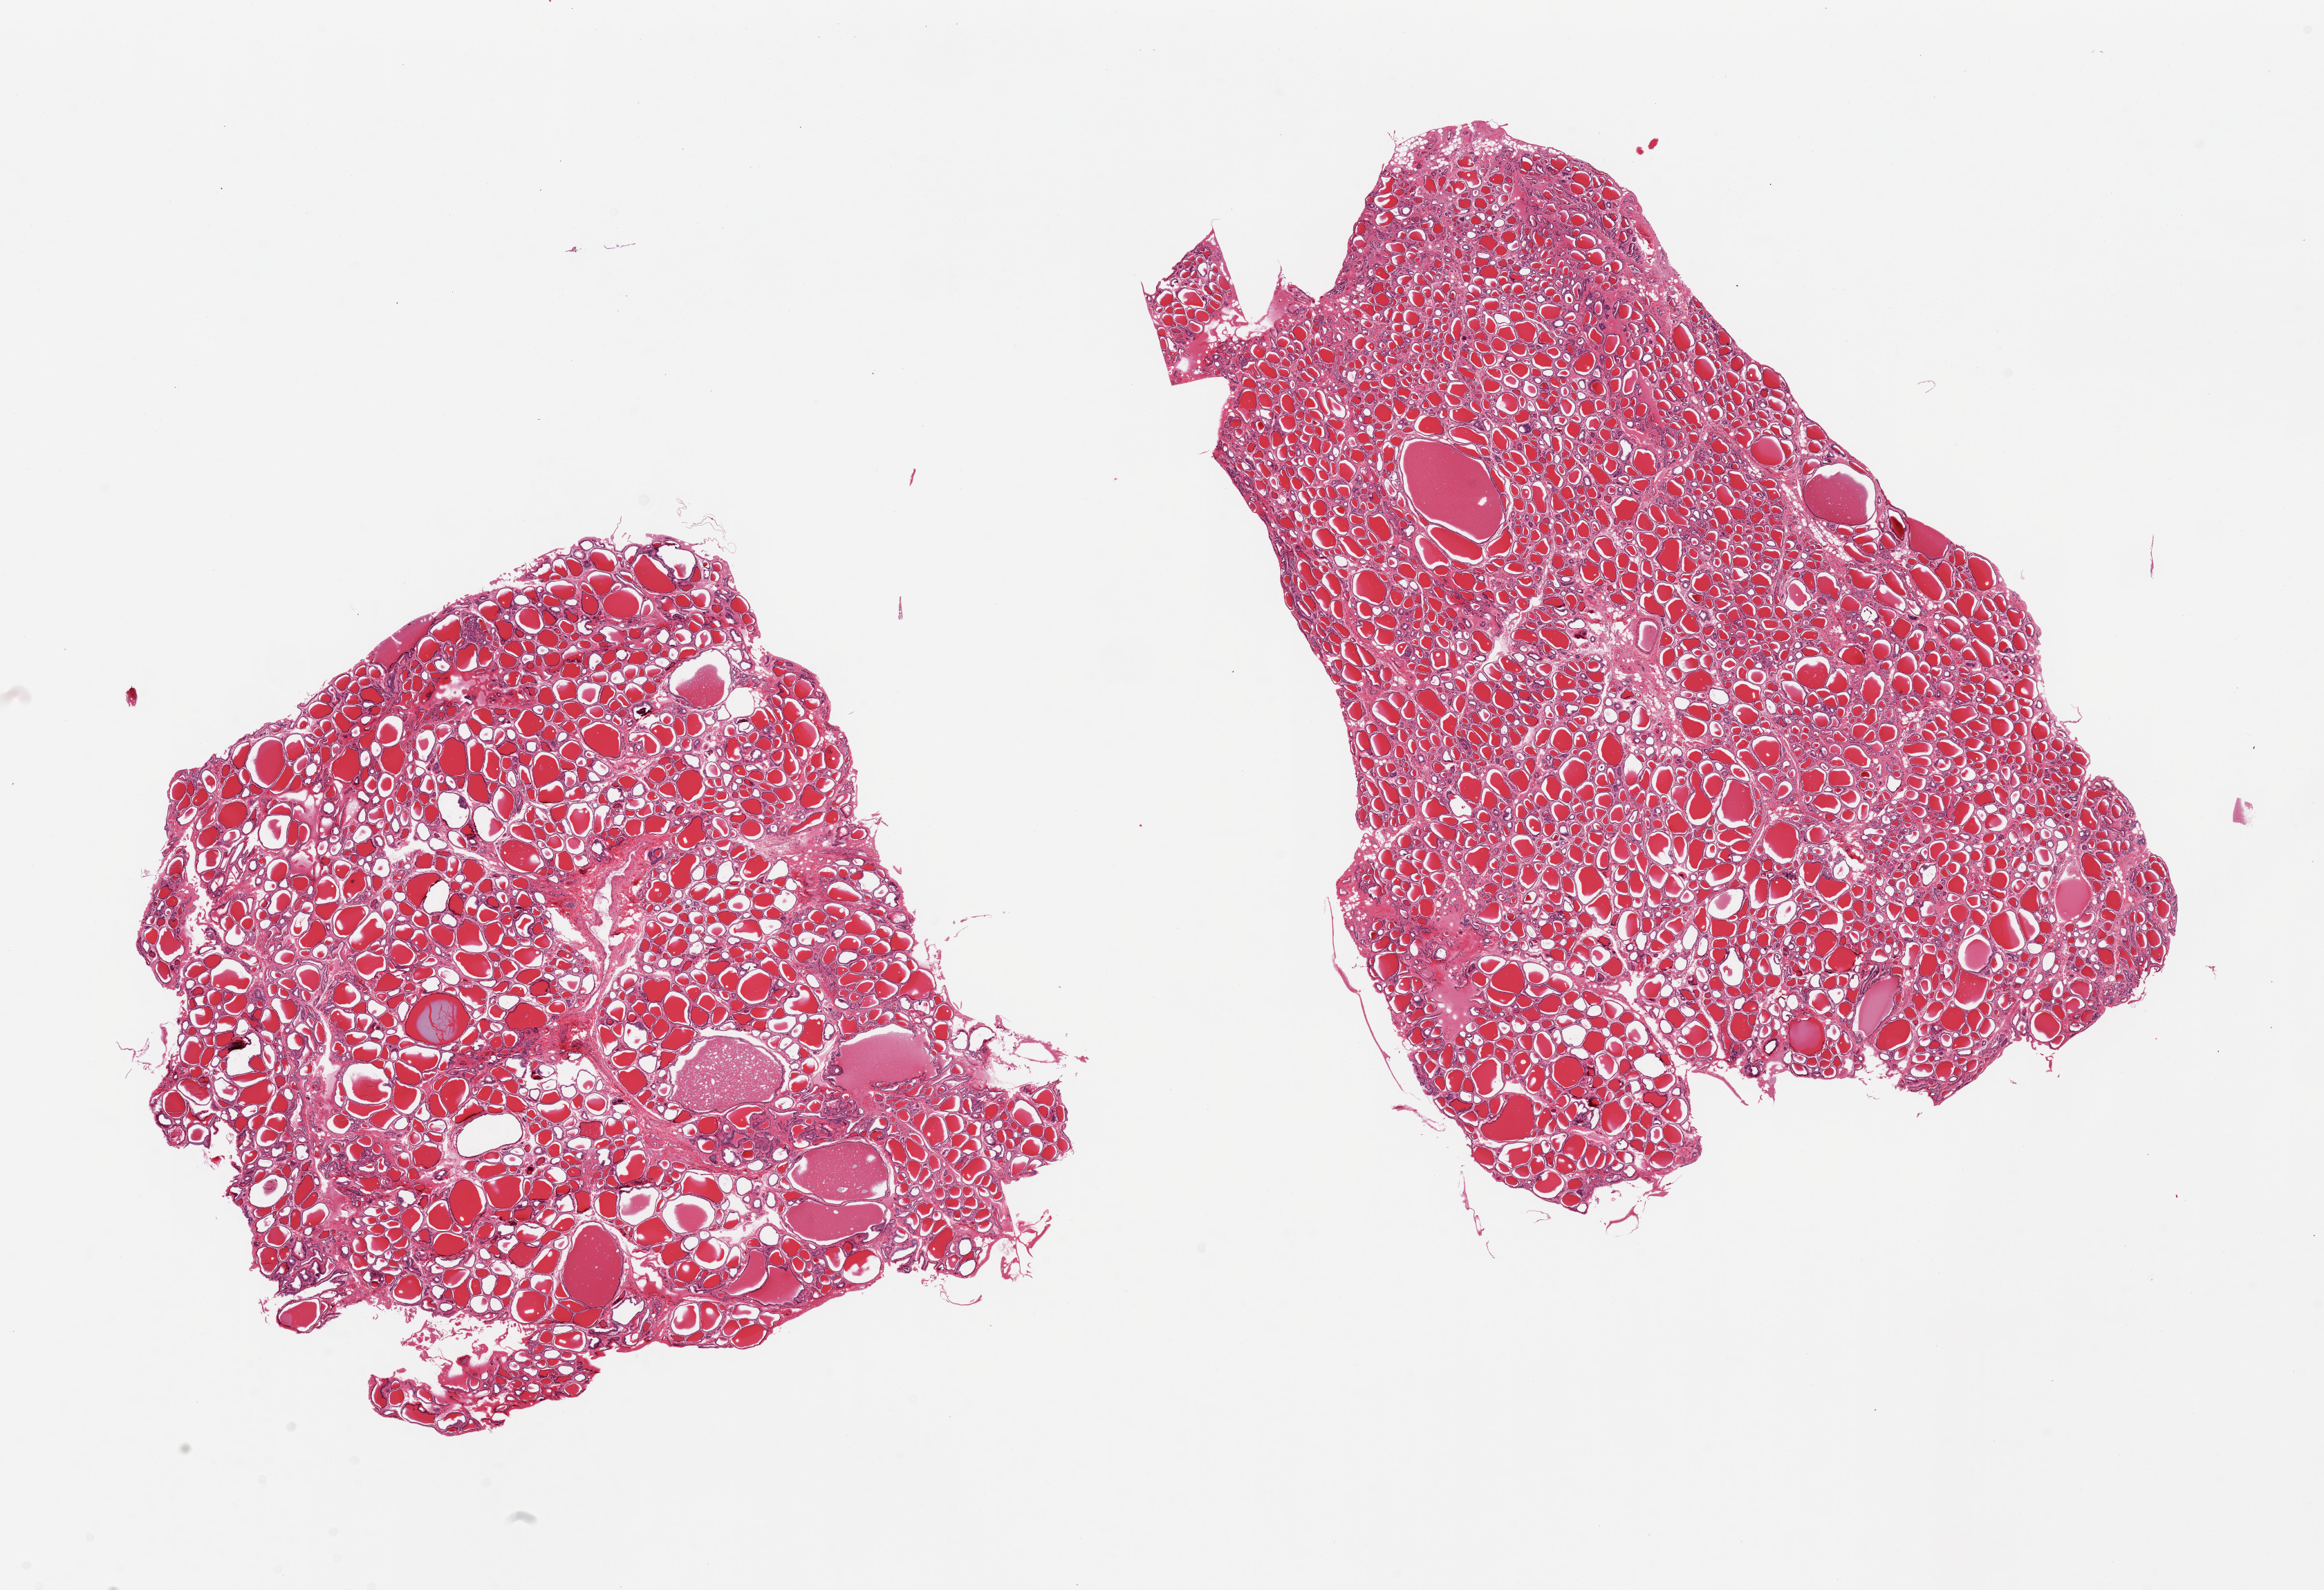
Digitized H&E-stained section — shown as a low-resolution overview of the whole scanned area (about 26.6 x 18.2 mm, acquisition: 20x scan). PAXgene-fixed, paraffin-embedded tissue. Target tissue: thyroid. Tissue donor sample. Donor sex: male.
- pathologist's review note for this sample: 2 pieces